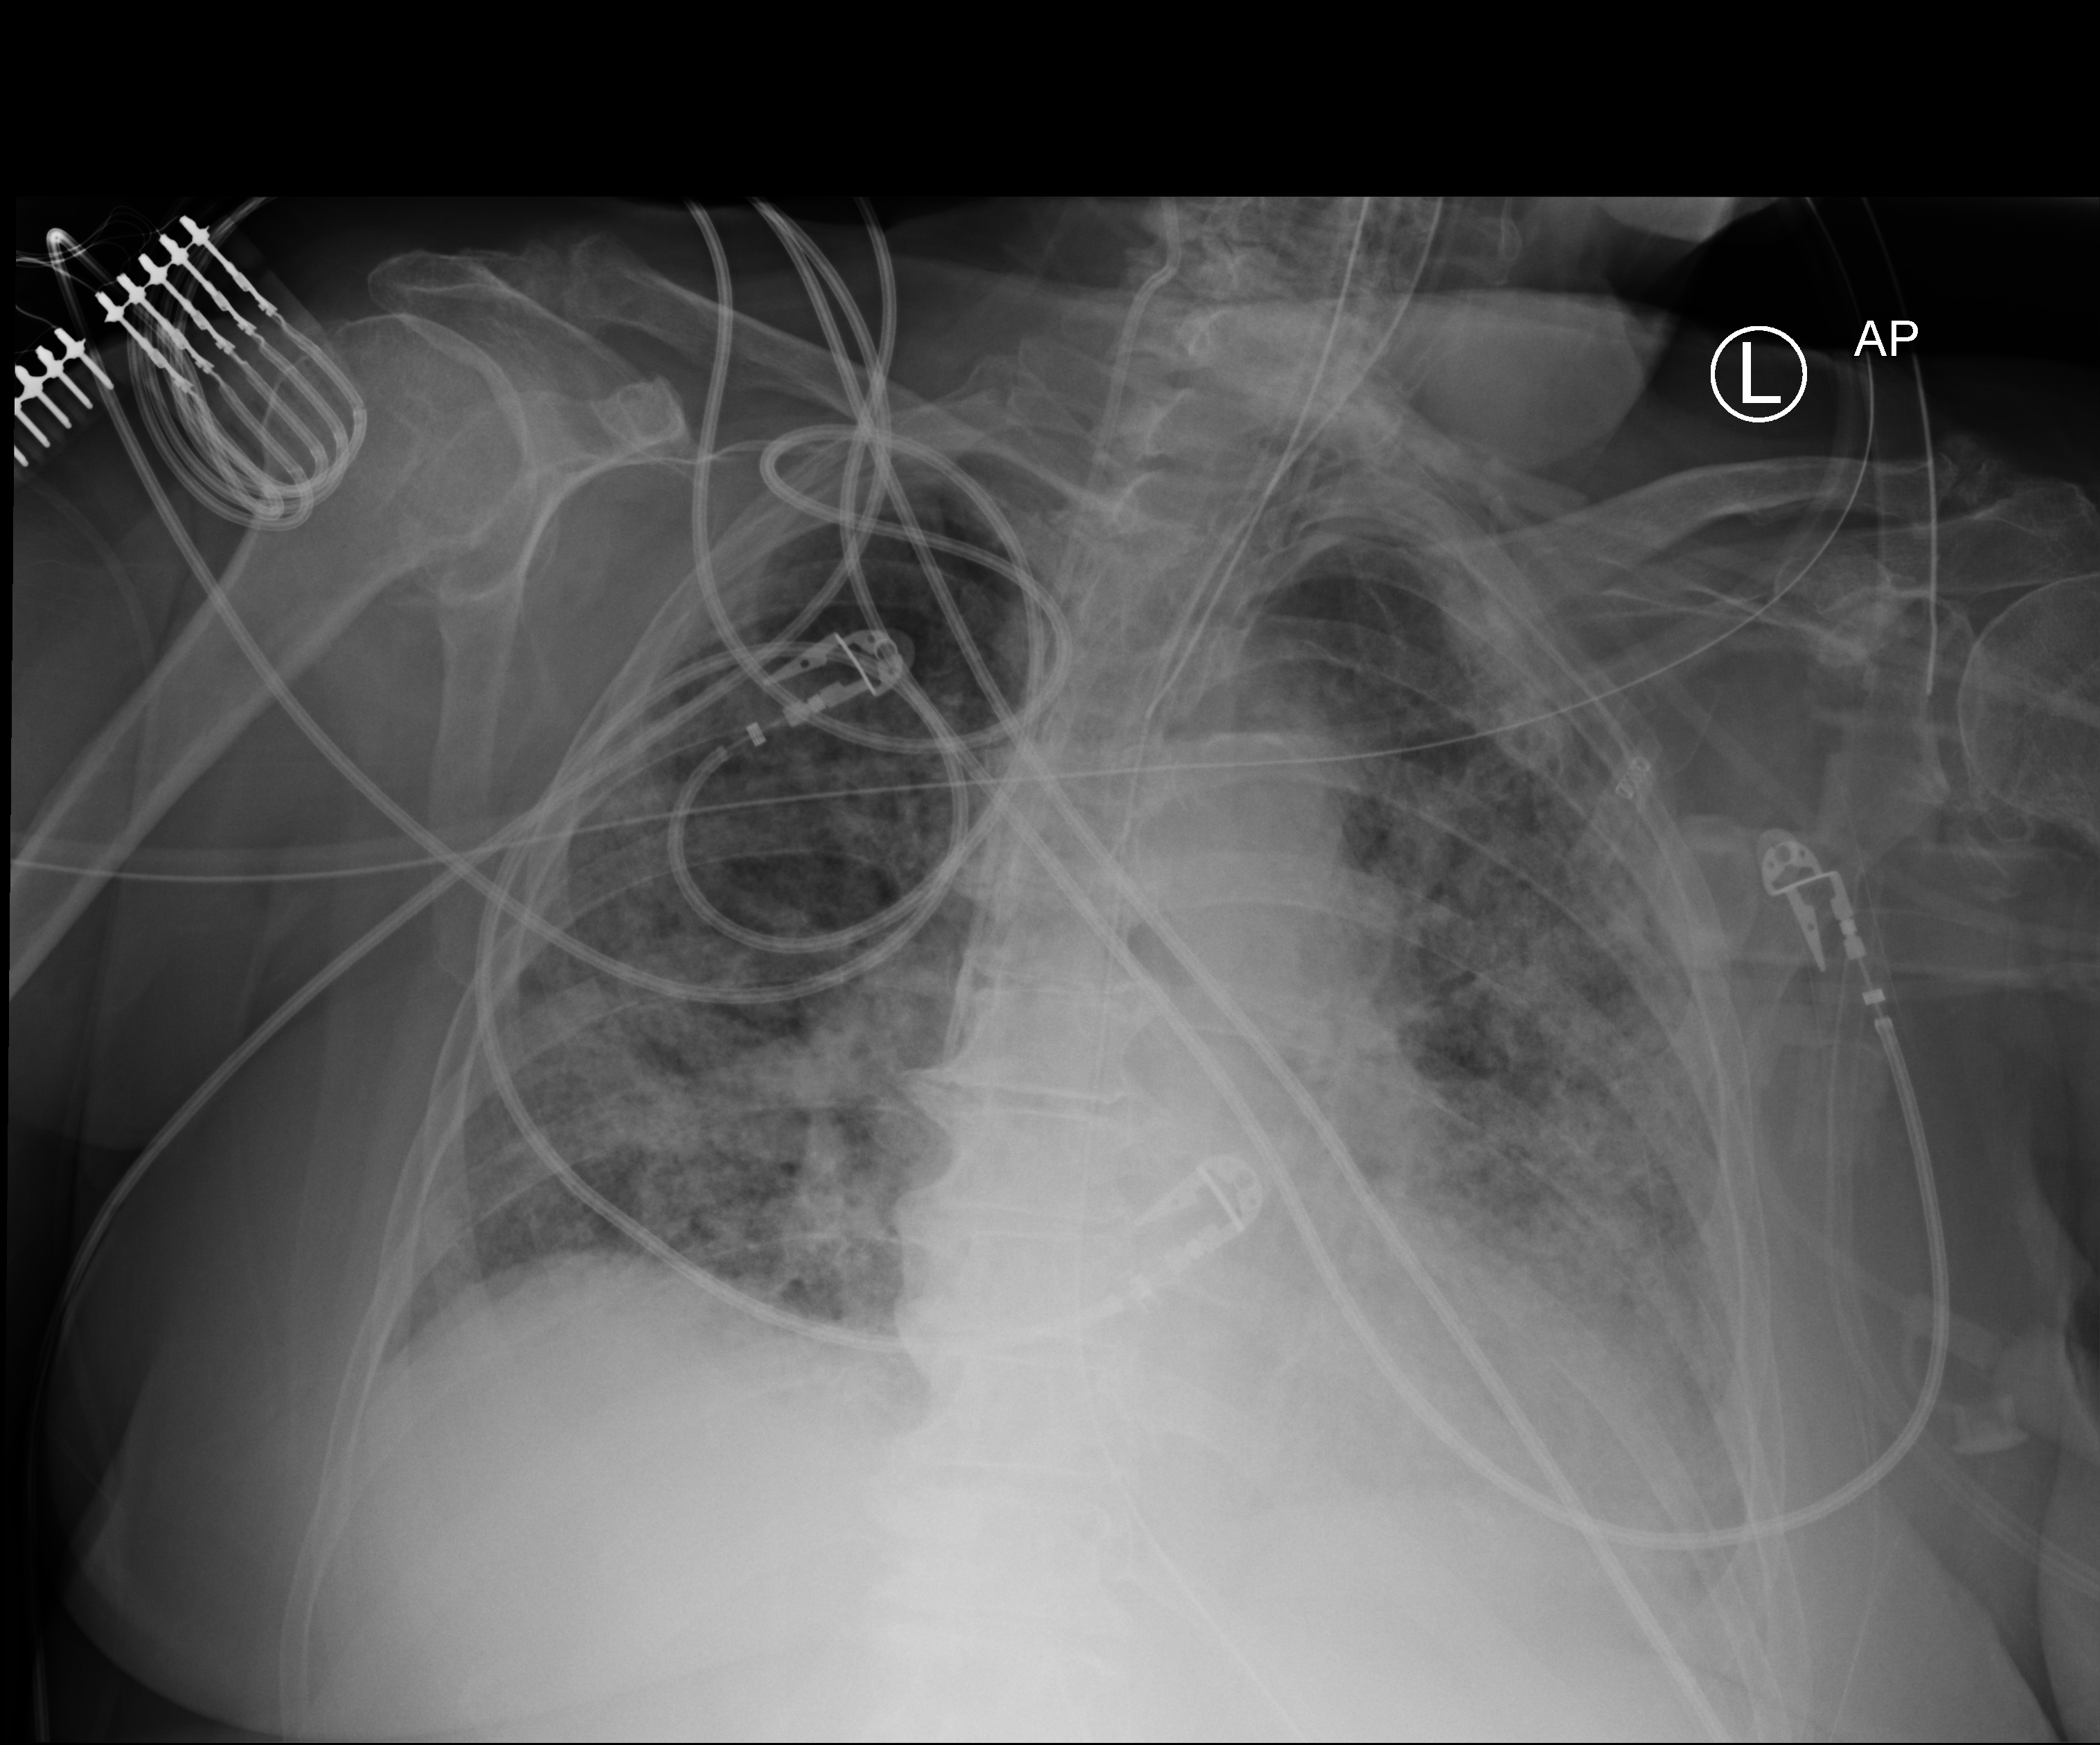
Bedside chest radiograph (computed radiography); anteroposterior (AP) projection. Female patient hospitalised with COVID-19, age 75–90 years.
Admission-level facts for this patient (not findings on this image; timing relative to this image not recorded): length of hospital stay: 56 days; admitted to intensive care during this hospital stay: no; mechanically ventilated during this hospital stay: yes.